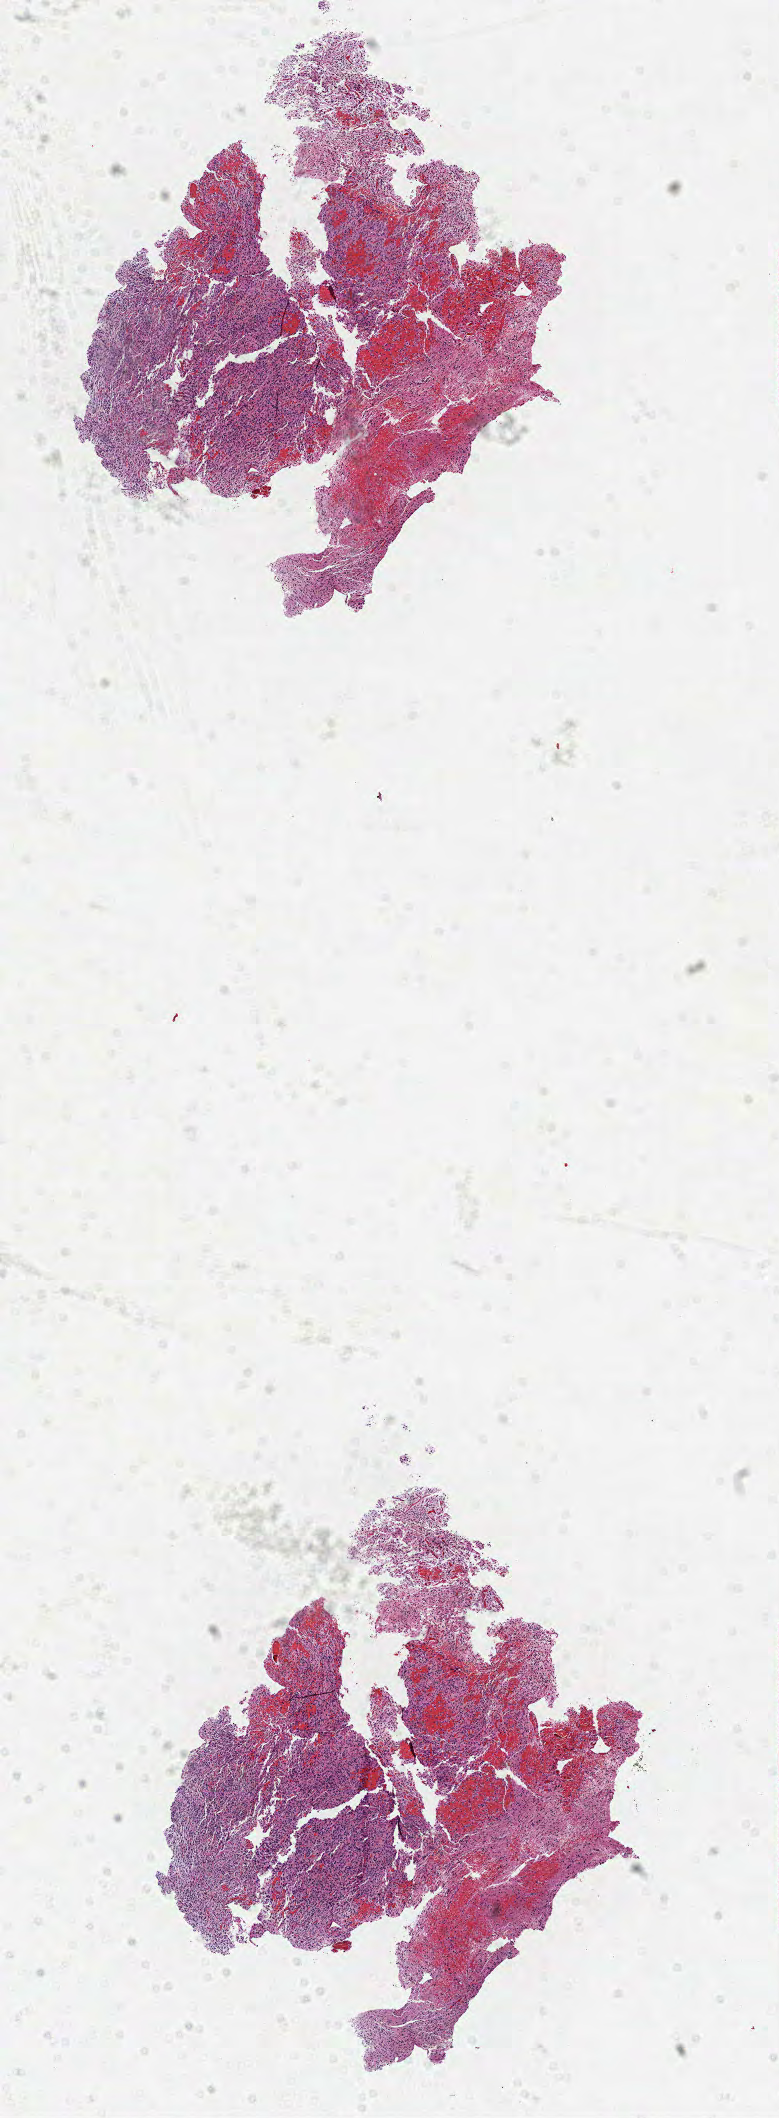
Whole-slide histology image, Hematoxylin and eosin (H&E) stained, low-resolution overview of the scanned area, about 6.3 x 17.1 mm (acquisition: 40x scan), formalin-fixed paraffin-embedded (FFPE) diagnostic section, brain, primary tumour sample. Patient: male, age at initial diagnosis 67 years.
Histologic diagnosis: Glioblastoma.